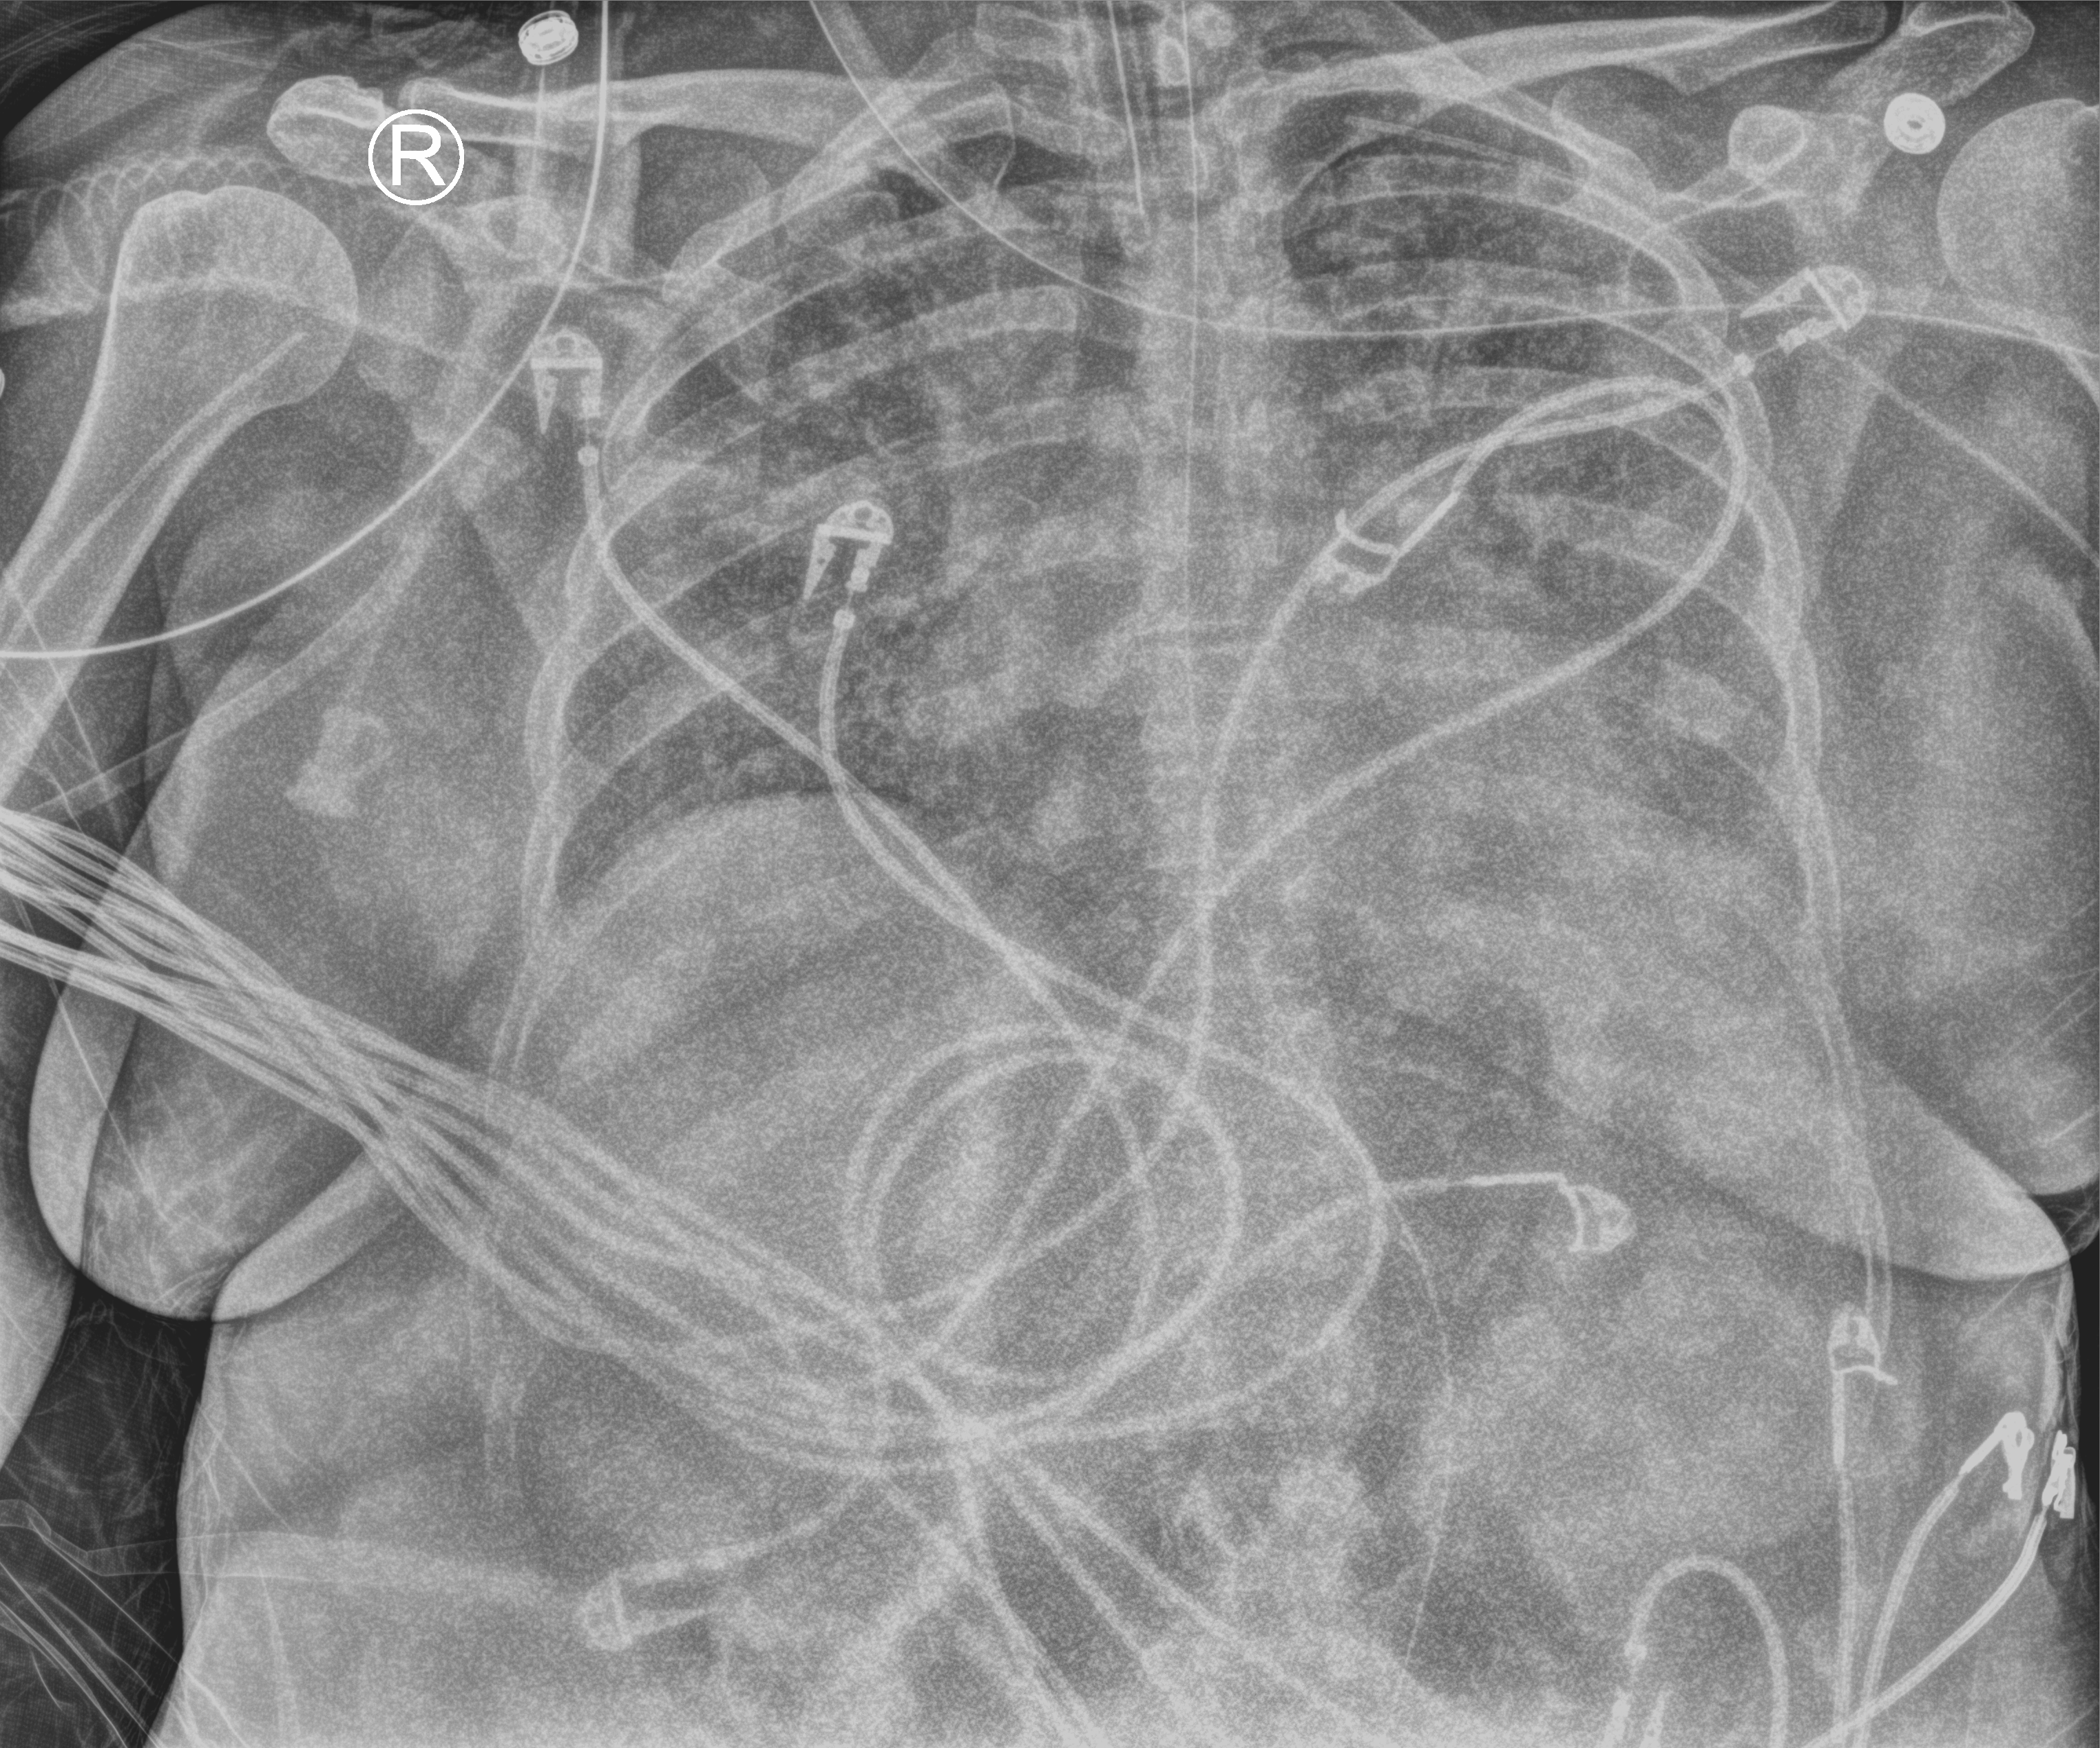
Bedside chest radiograph (computed radiography); anteroposterior (AP) projection. Female patient hospitalised with COVID-19, age 18–59 years.
Admission-level facts for this patient (not findings on this image; timing relative to this image not recorded): admitted to intensive care during this hospital stay: yes; mechanically ventilated during this hospital stay: yes.